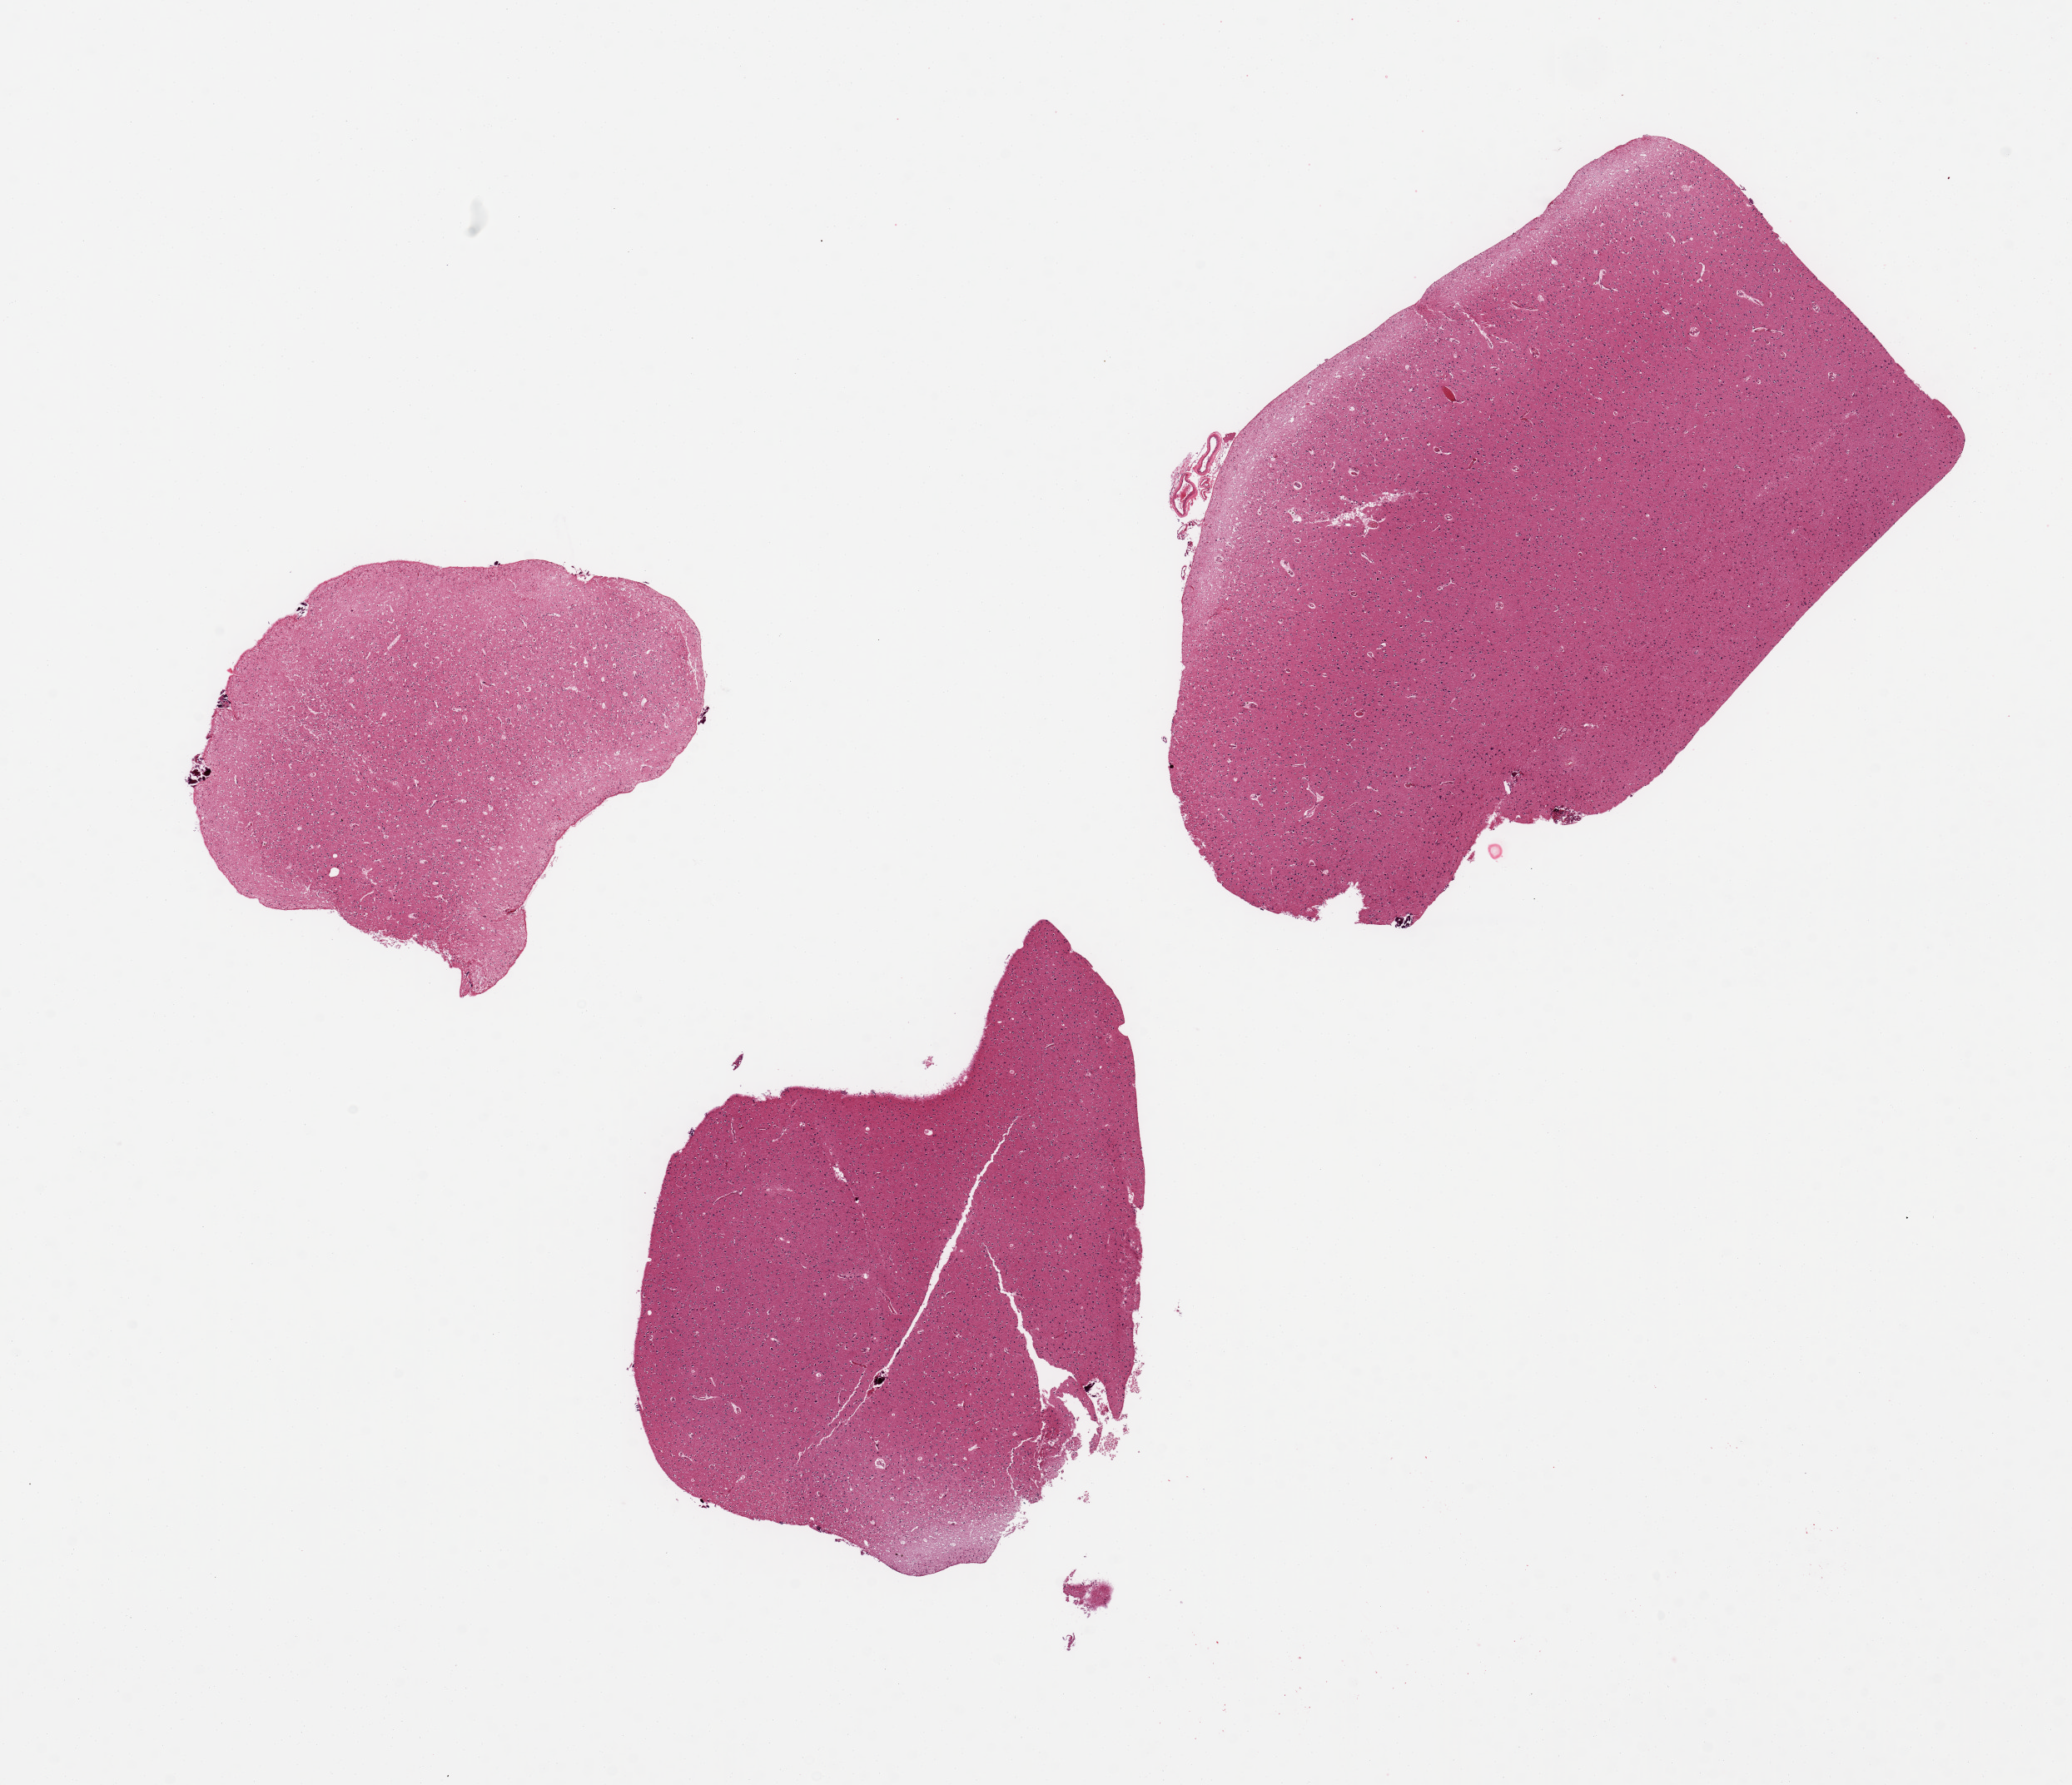
Haematoxylin and eosin whole-slide image — a low-resolution overview of the entire scanned area, about 19.7 x 17.0 mm (slide scanned at 20x), PAXgene-fixed paraffin-embedded (PFPE) section, section of cerebral cortex (target tissue), tissue donor sample. Male donor.
* pathologist's review note for this sample: 3 pieces, no abnormalities